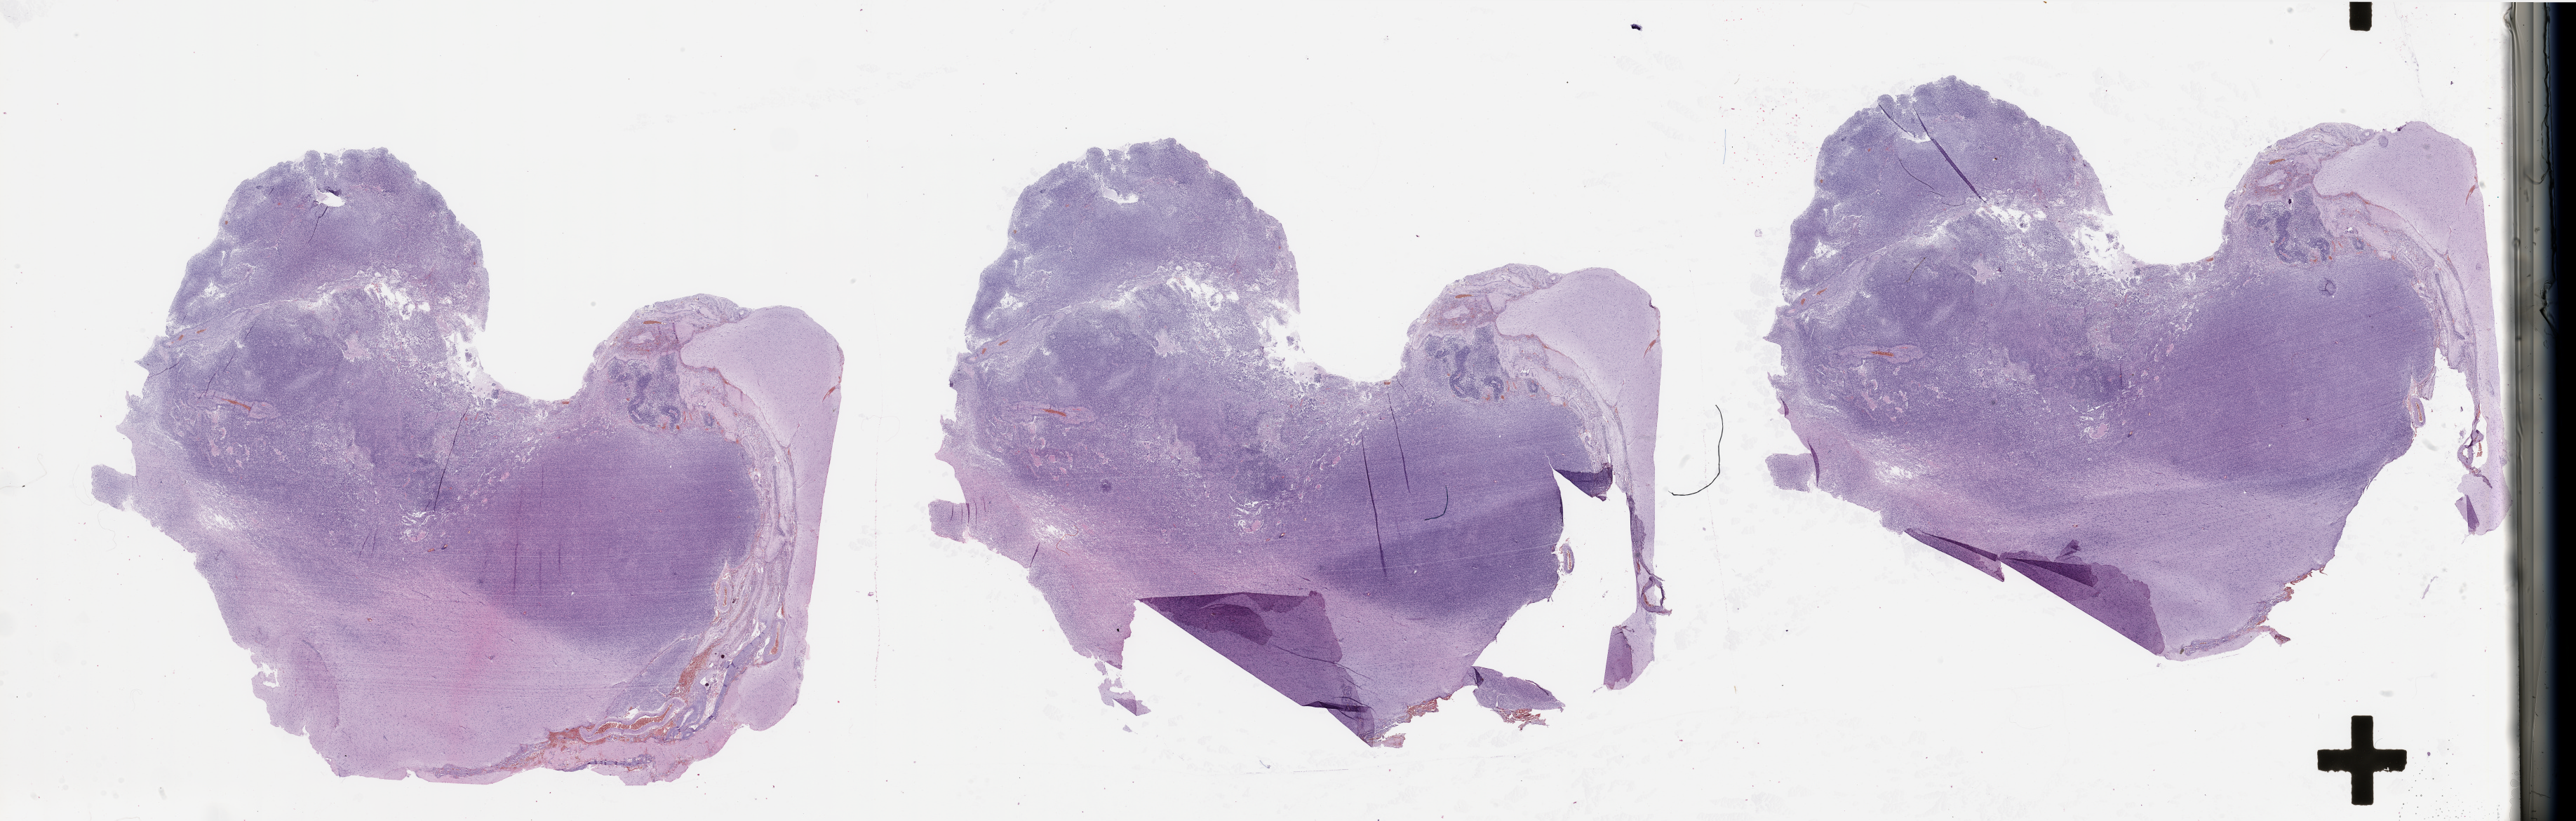
Whole-slide histology image, H&E-stained, a low-resolution overview of the entire scanned area, about 58.1 x 18.5 mm. Tumour tissue sample, sampled site: brain. Male, 81 y/o. Composition of this section per pathologist review: tumour nuclei 60%, necrosis 7%.
- histologic diagnosis: Glioblastoma
- primary tumour site (as recorded): temporal lobe